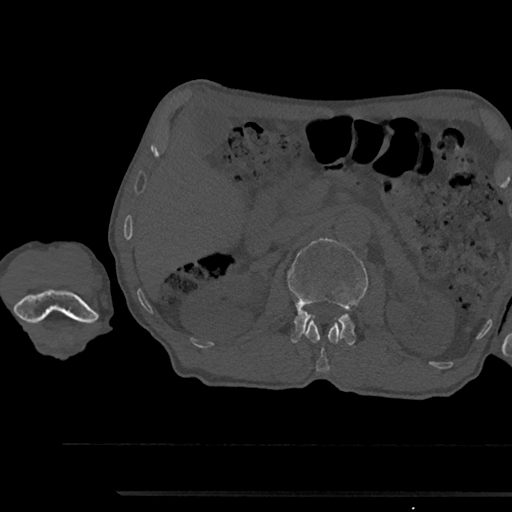
CT including the spine, one axial slice. Position 598 of 797 along the scan axis. Reconstruction kernel Br40s/3. Bone window (W 1800 / L 400 HU). 0.5 mm slice thickness. 512 × 512 image matrix, field of view 367 × 367 mm. Male patient, age 79 years. Case-level facts recorded for this patient, not image findings: primary cancer: prostate.
Structures marked on this image (semi-automatic segmentation, software-assisted and operator-edited):
- L1 vertebra: box from (x=305, y=320) to (x=343, y=371) px
- L2 vertebra: (x=288, y=238)–(x=368, y=345)